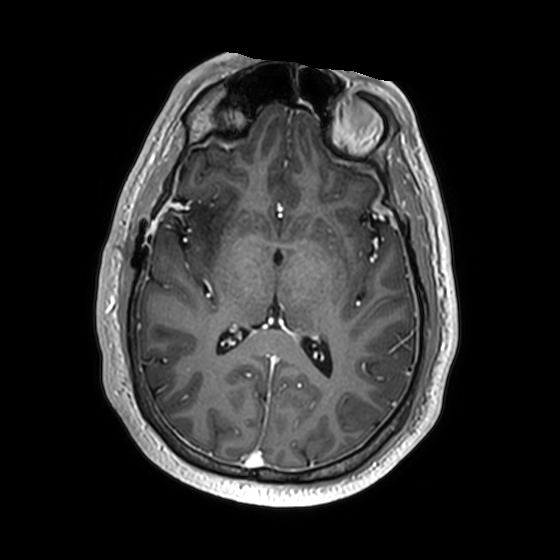
Brain MRI from a brain-tumour surgery series, one axial slice. T1-weighted post-contrast. 1 mm slice thickness. 560 × 560 image matrix, field of view 256 × 256 mm. Case-level facts recorded for this patient, not image findings: histopathology: Astrocytoma; WHO grade: 2; IDH mutation: yes.
Outlined on this slice (expert manual segmentation):
- previous resection cavity: bounding box <177,198,187,205> (left, top, right, bottom; pixels)